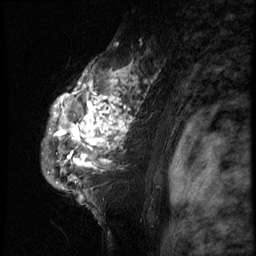
Breast MRI (dynamic contrast-enhanced), one sagittal slice; slice 52 of 66 in the series (ordered by position); 3 images stored at this slice position (order not interpretable as contrast timing); 1.5 T; TE 4.2 ms, TR 8.9 ms; 2.5 mm slice thickness; 256 × 256 image matrix, field of view 200 × 200 mm. Female patient, age 39 years. Case-level facts recorded for this patient, not image findings: setting: breast cancer imaged before/during neoadjuvant chemotherapy; receptor status: HER2-positive.
Structures marked on this image (semi-automatic segmentation, software-assisted and operator-edited):
- analysis volume of interest (the breast-tissue region the enhancement analysis was run in; not a lesion): bounding box <40,44,166,196> (left, top, right, bottom; pixels)
- tumour enhancement mask (voxels above the 140 % enhancement threshold inside the analysis volume of interest): <55,63,156,171>